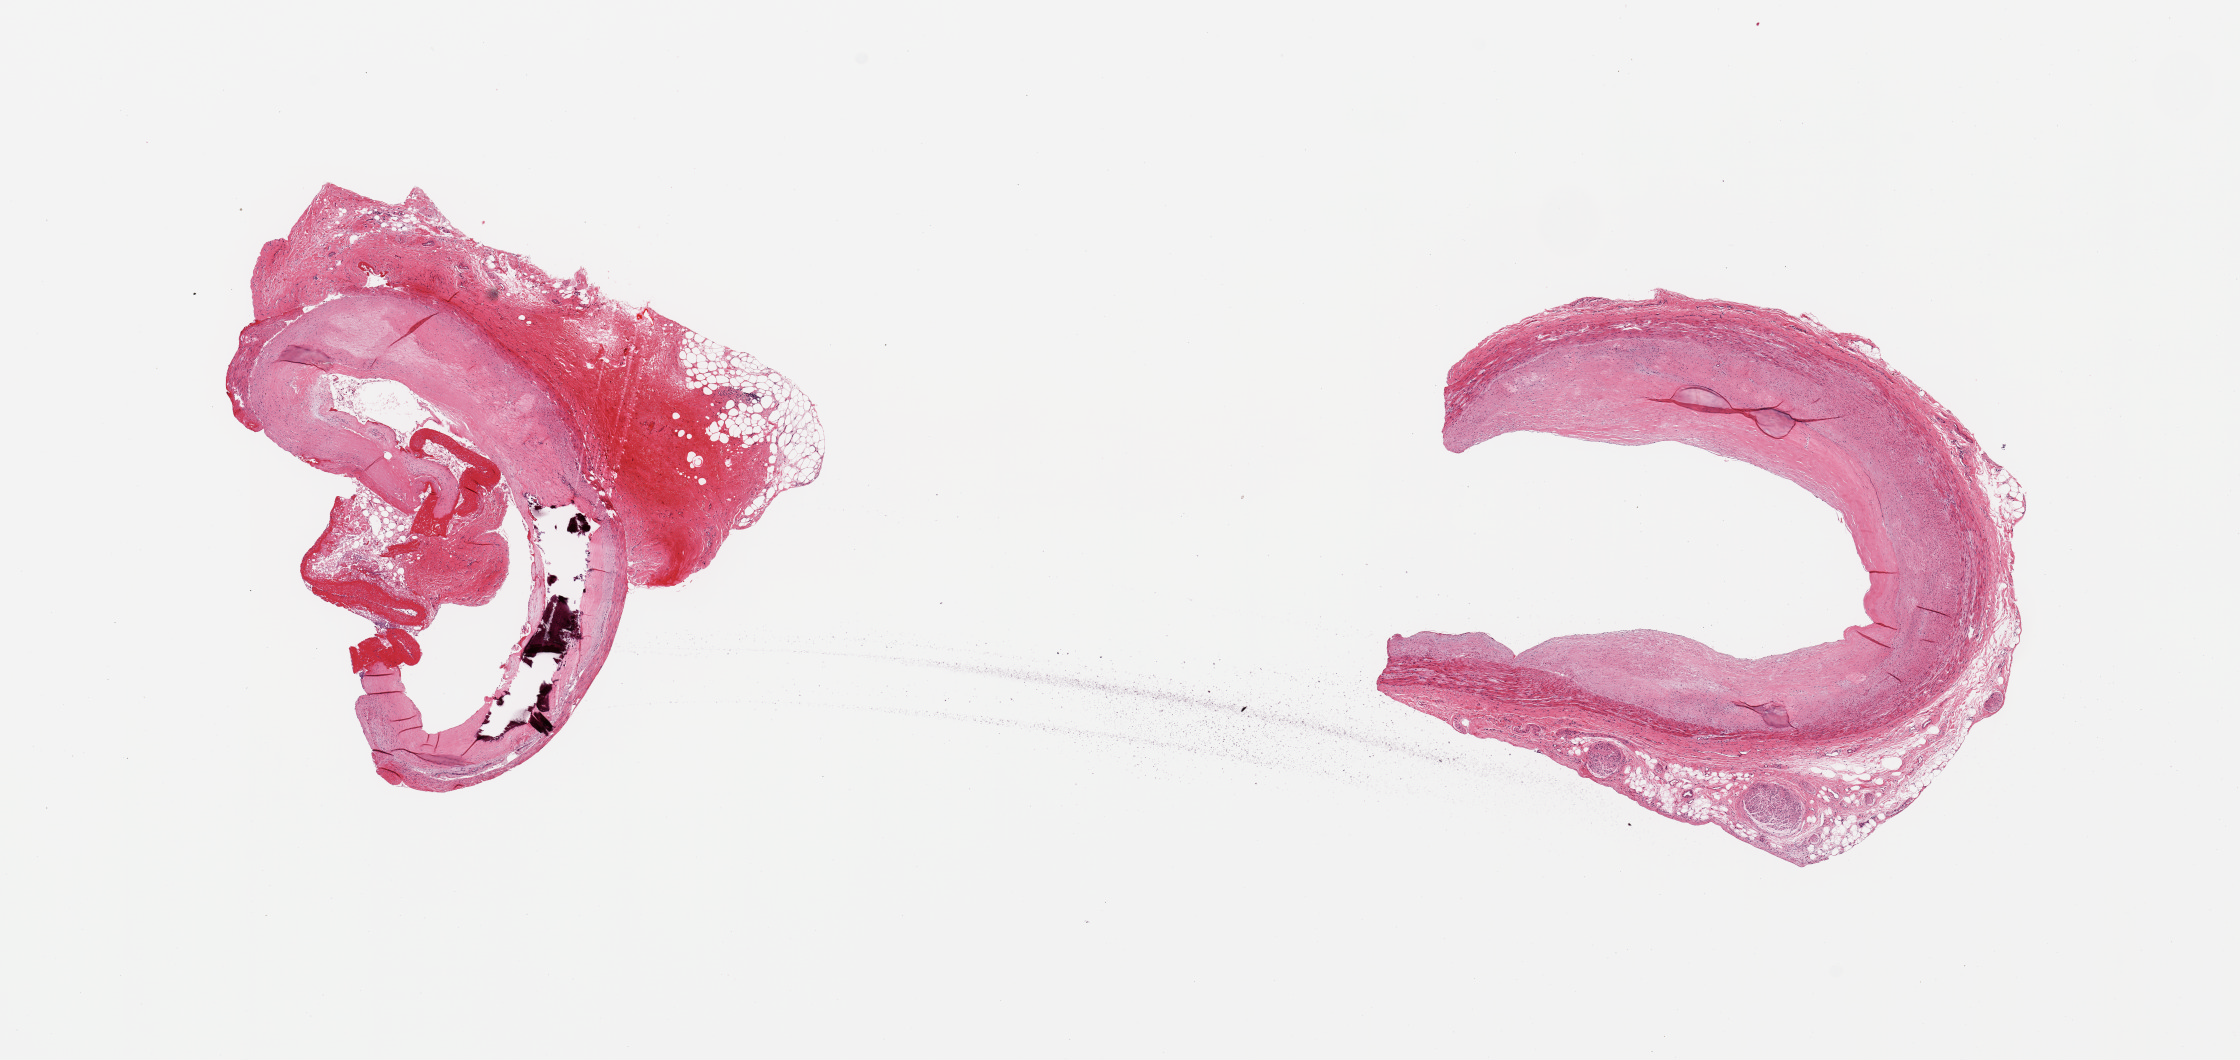
Digitized haematoxylin and eosin-stained section, whole scanned area (about 17.7 x 8.4 mm) shown as a low-resolution overview; PAXgene-fixed paraffin-embedded (PFPE) section; section of coronary artery (target tissue); donor tissue sample. Donor sex: male.
Review note (as recorded): 2 pieces ~50-60% occluive focally calcified (del0.ineated) atherosis.